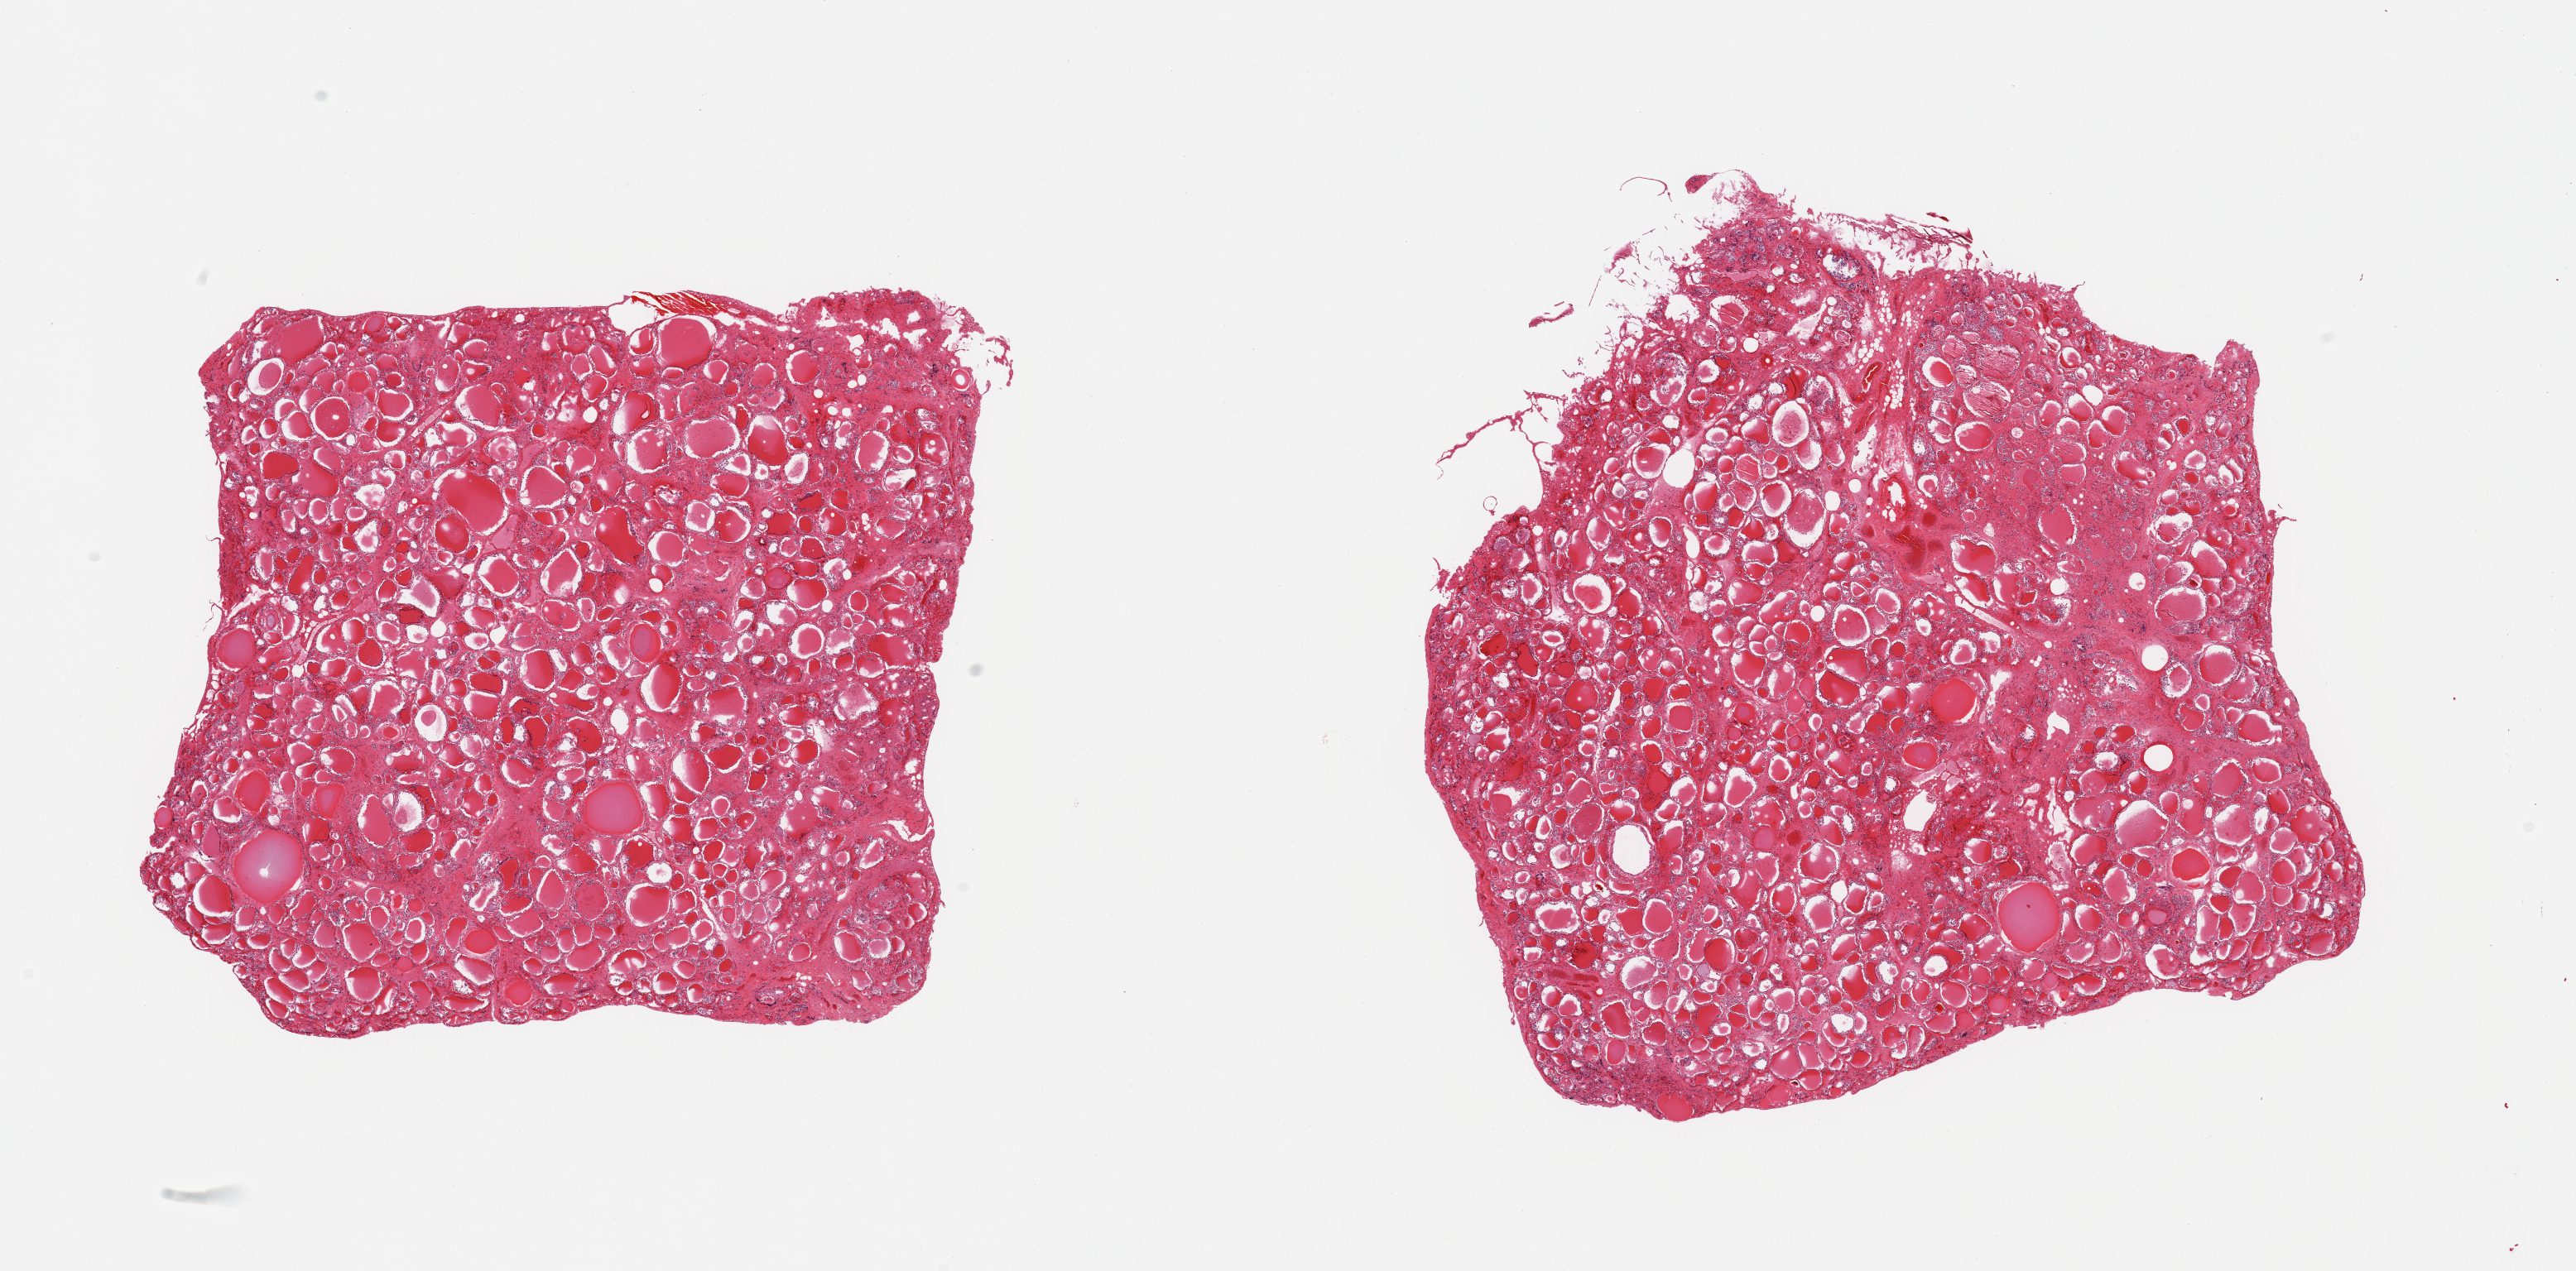
H&E whole-slide image, shown as a low-resolution overview of the whole scanned area (about 24.6 x 12.1 mm), PAXgene-fixed paraffin-embedded (PFPE) section, target tissue: thyroid, tissue donor sample. Donor sex: male.
Pathologist's review note for this sample: 2 pieces.